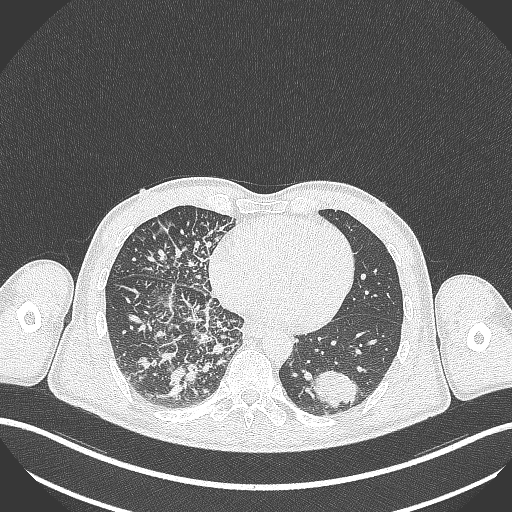
Chest CT, one axial slice. Slice 107 of 348 in the series (ordered by position). Lung window (W 1500 / L -600 HU). 1 mm slice thickness. 512 × 512 image matrix. Male patient, age 49 years. Case-level facts recorded for this patient, not image findings: clinical TNM (as recorded): T2b N1 M0.
Structures marked on this image (bounding box drawn by a radiologist):
- lung tumour (recorded histology: adenocarcinoma): box from (x=309, y=366) to (x=358, y=408) px